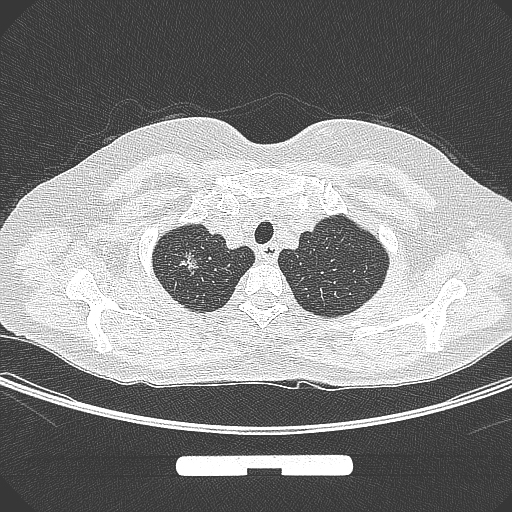
Chest CT, one axial slice; position 260 of 295 along the scan axis; lung window (W 1500 / L -600 HU); 1 mm slice thickness; 512 × 512 image matrix, field of view 369 × 369 mm. Female patient, age 58 years. Case-level facts recorded for this patient, not image findings: clinical TNM (as recorded): T1b N0 M0; histopathological grade: G2-3.
Outlined on this slice (rectangle marked by the reading radiologist):
- lung tumour (recorded histology: adenocarcinoma): bounding box (x1, y1, x2, y2) in pixels: (177, 248, 207, 284)